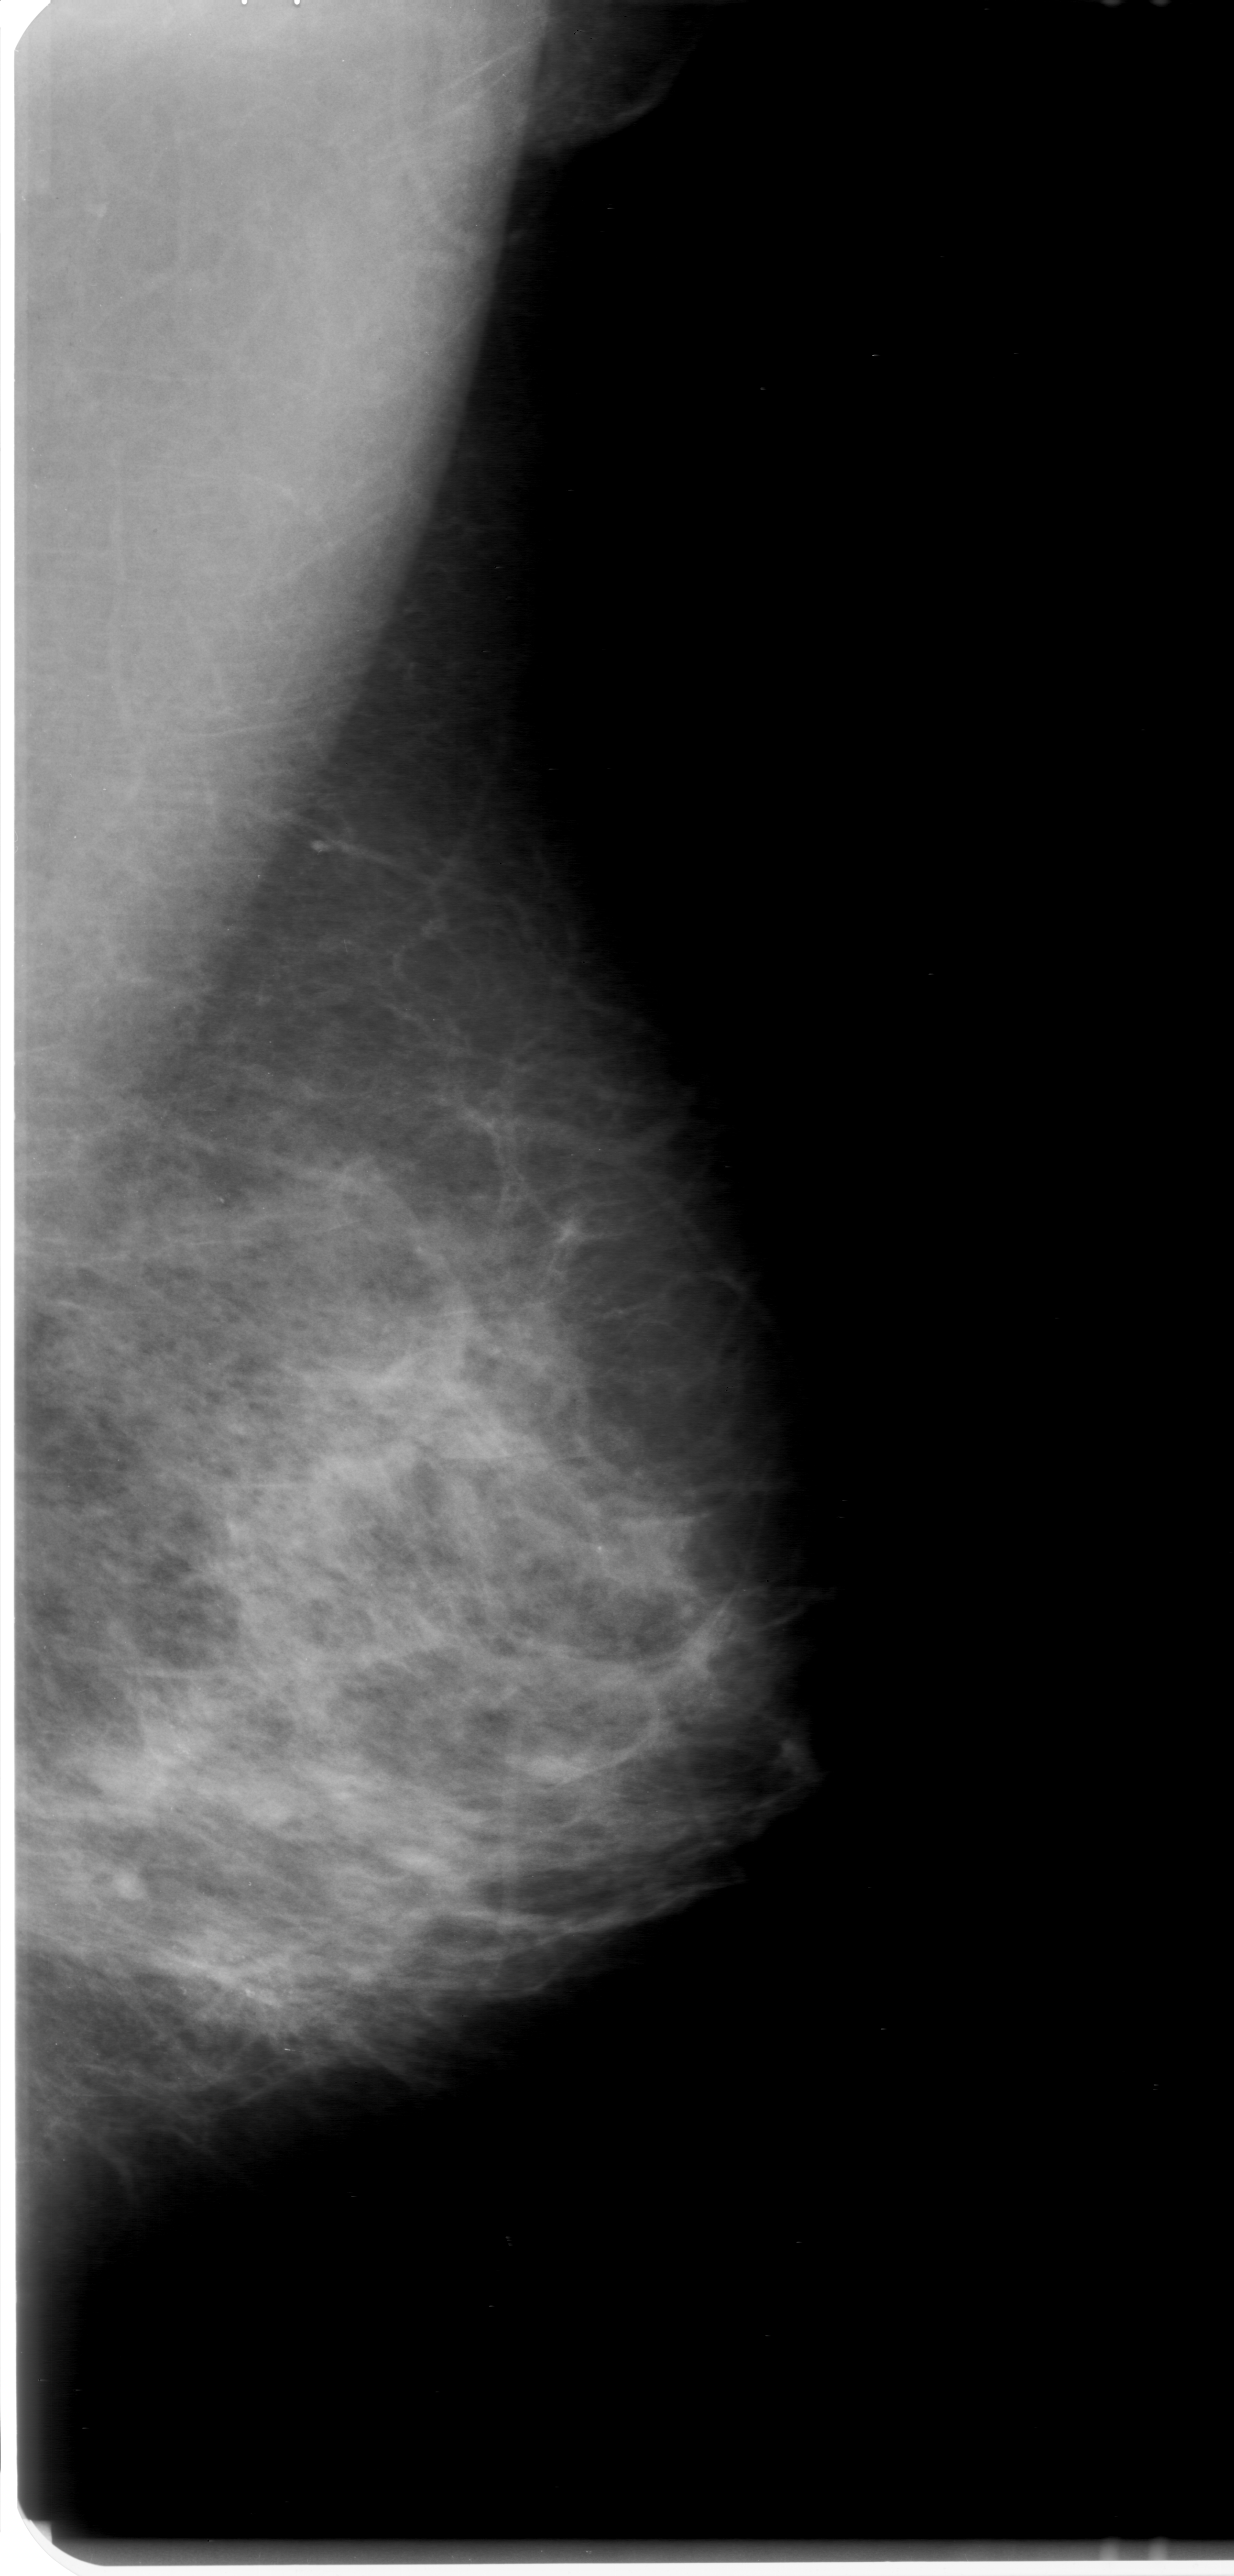
Digitized screen-film mammogram, left breast, mediolateral oblique (MLO) view.
- Radiologist-marked abnormalities on this image: calcifications, morphology pleomorphic, distribution clustered; BI-RADS assessment category 0 (incomplete: needs additional imaging); pathology (as recorded): malignant.